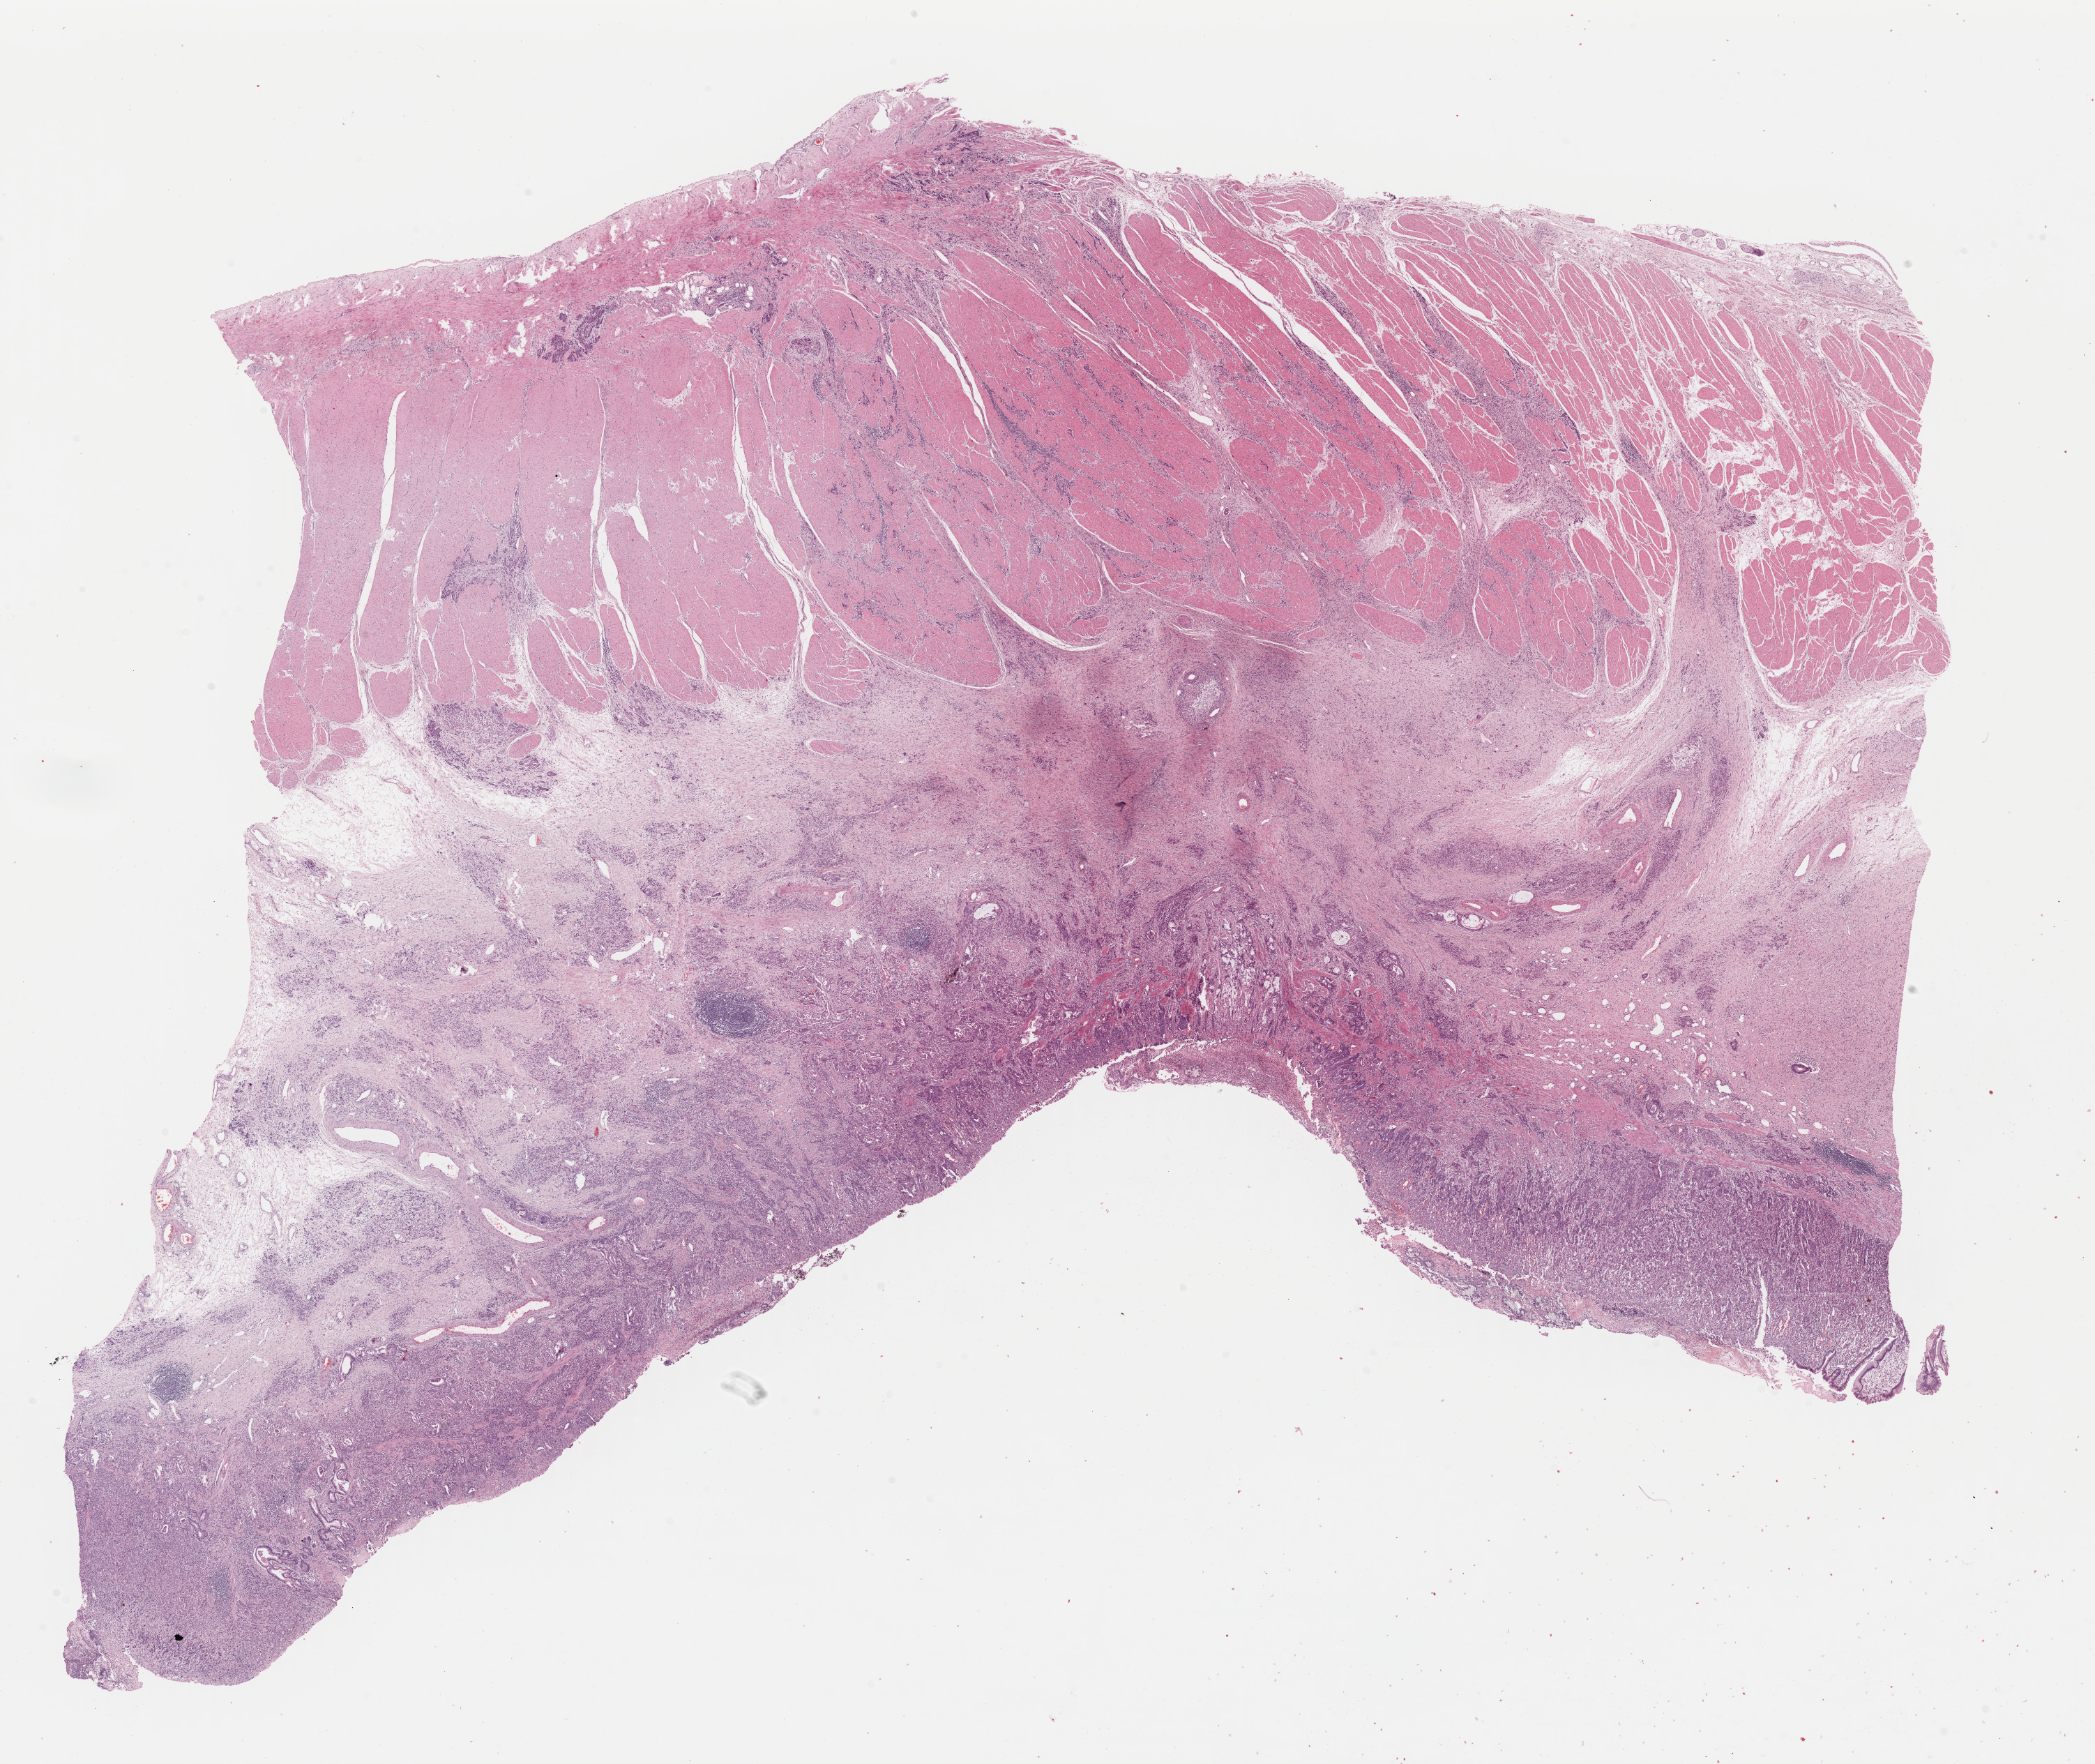
Whole-slide histology image, Hematoxylin and eosin (H&E) stained, a low-resolution overview of the entire scanned area, about 23.7 x 20.0 mm (slide scanned at 40x); formalin-fixed paraffin-embedded (FFPE) diagnostic section; primary tumour sample from the stomach. Patient: female, age at initial diagnosis 66 years. Histologic grade: G2 (moderately differentiated).
Pathologic diagnosis: Adenocarcinoma, intestinal type (gastric antrum). AJCC pathologic stage: IIB (7th edition). Lymph nodes positive (case pathology): 4 of 14 examined.